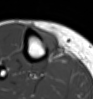
MRI of an extremity soft-tissue mass, one axial slice; slice 18 of 54 in the series (ordered by position); MR volume resampled by the dataset authors to the PET/CT grid (not the native acquisition matrix); 3.27 mm slice thickness; 93 × 99 image matrix. Female patient. Case-level facts recorded for this patient, not image findings: histological type: undifferentiated – high grade; grade: high; site of the primary tumour: right thigh.
Annotated regions visible in this slice (expert contour drawn on MRI and transferred to this co-registered scan by the dataset authors):
- gross tumour volume (mass): bounding box [x1, y1, x2, y2] px = [36, 29, 60, 58]